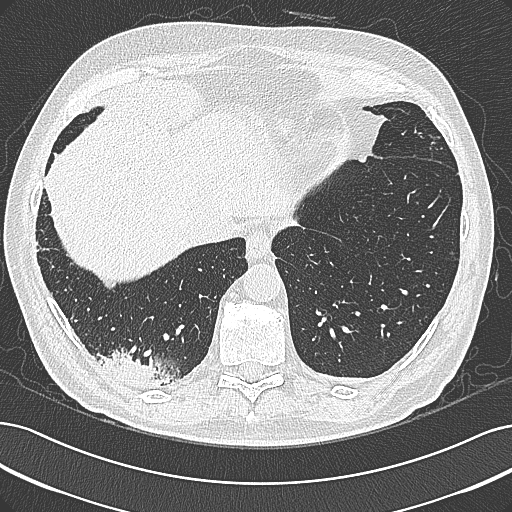
Chest CT (low-dose screening protocol), one axial image; first (baseline) screen; lung window (W 1500 / L -600 HU); 1 mm slice thickness; lung (sharp) reconstruction kernel (B80f); slice 234 of 355 in the series. Male, age 68 years at enrolment.
Expert reader's lesion annotation, box from (x=97, y=340) to (x=186, y=401) px. Screening reader's record for this exam: no non-calcified nodule ≥4 mm recorded.